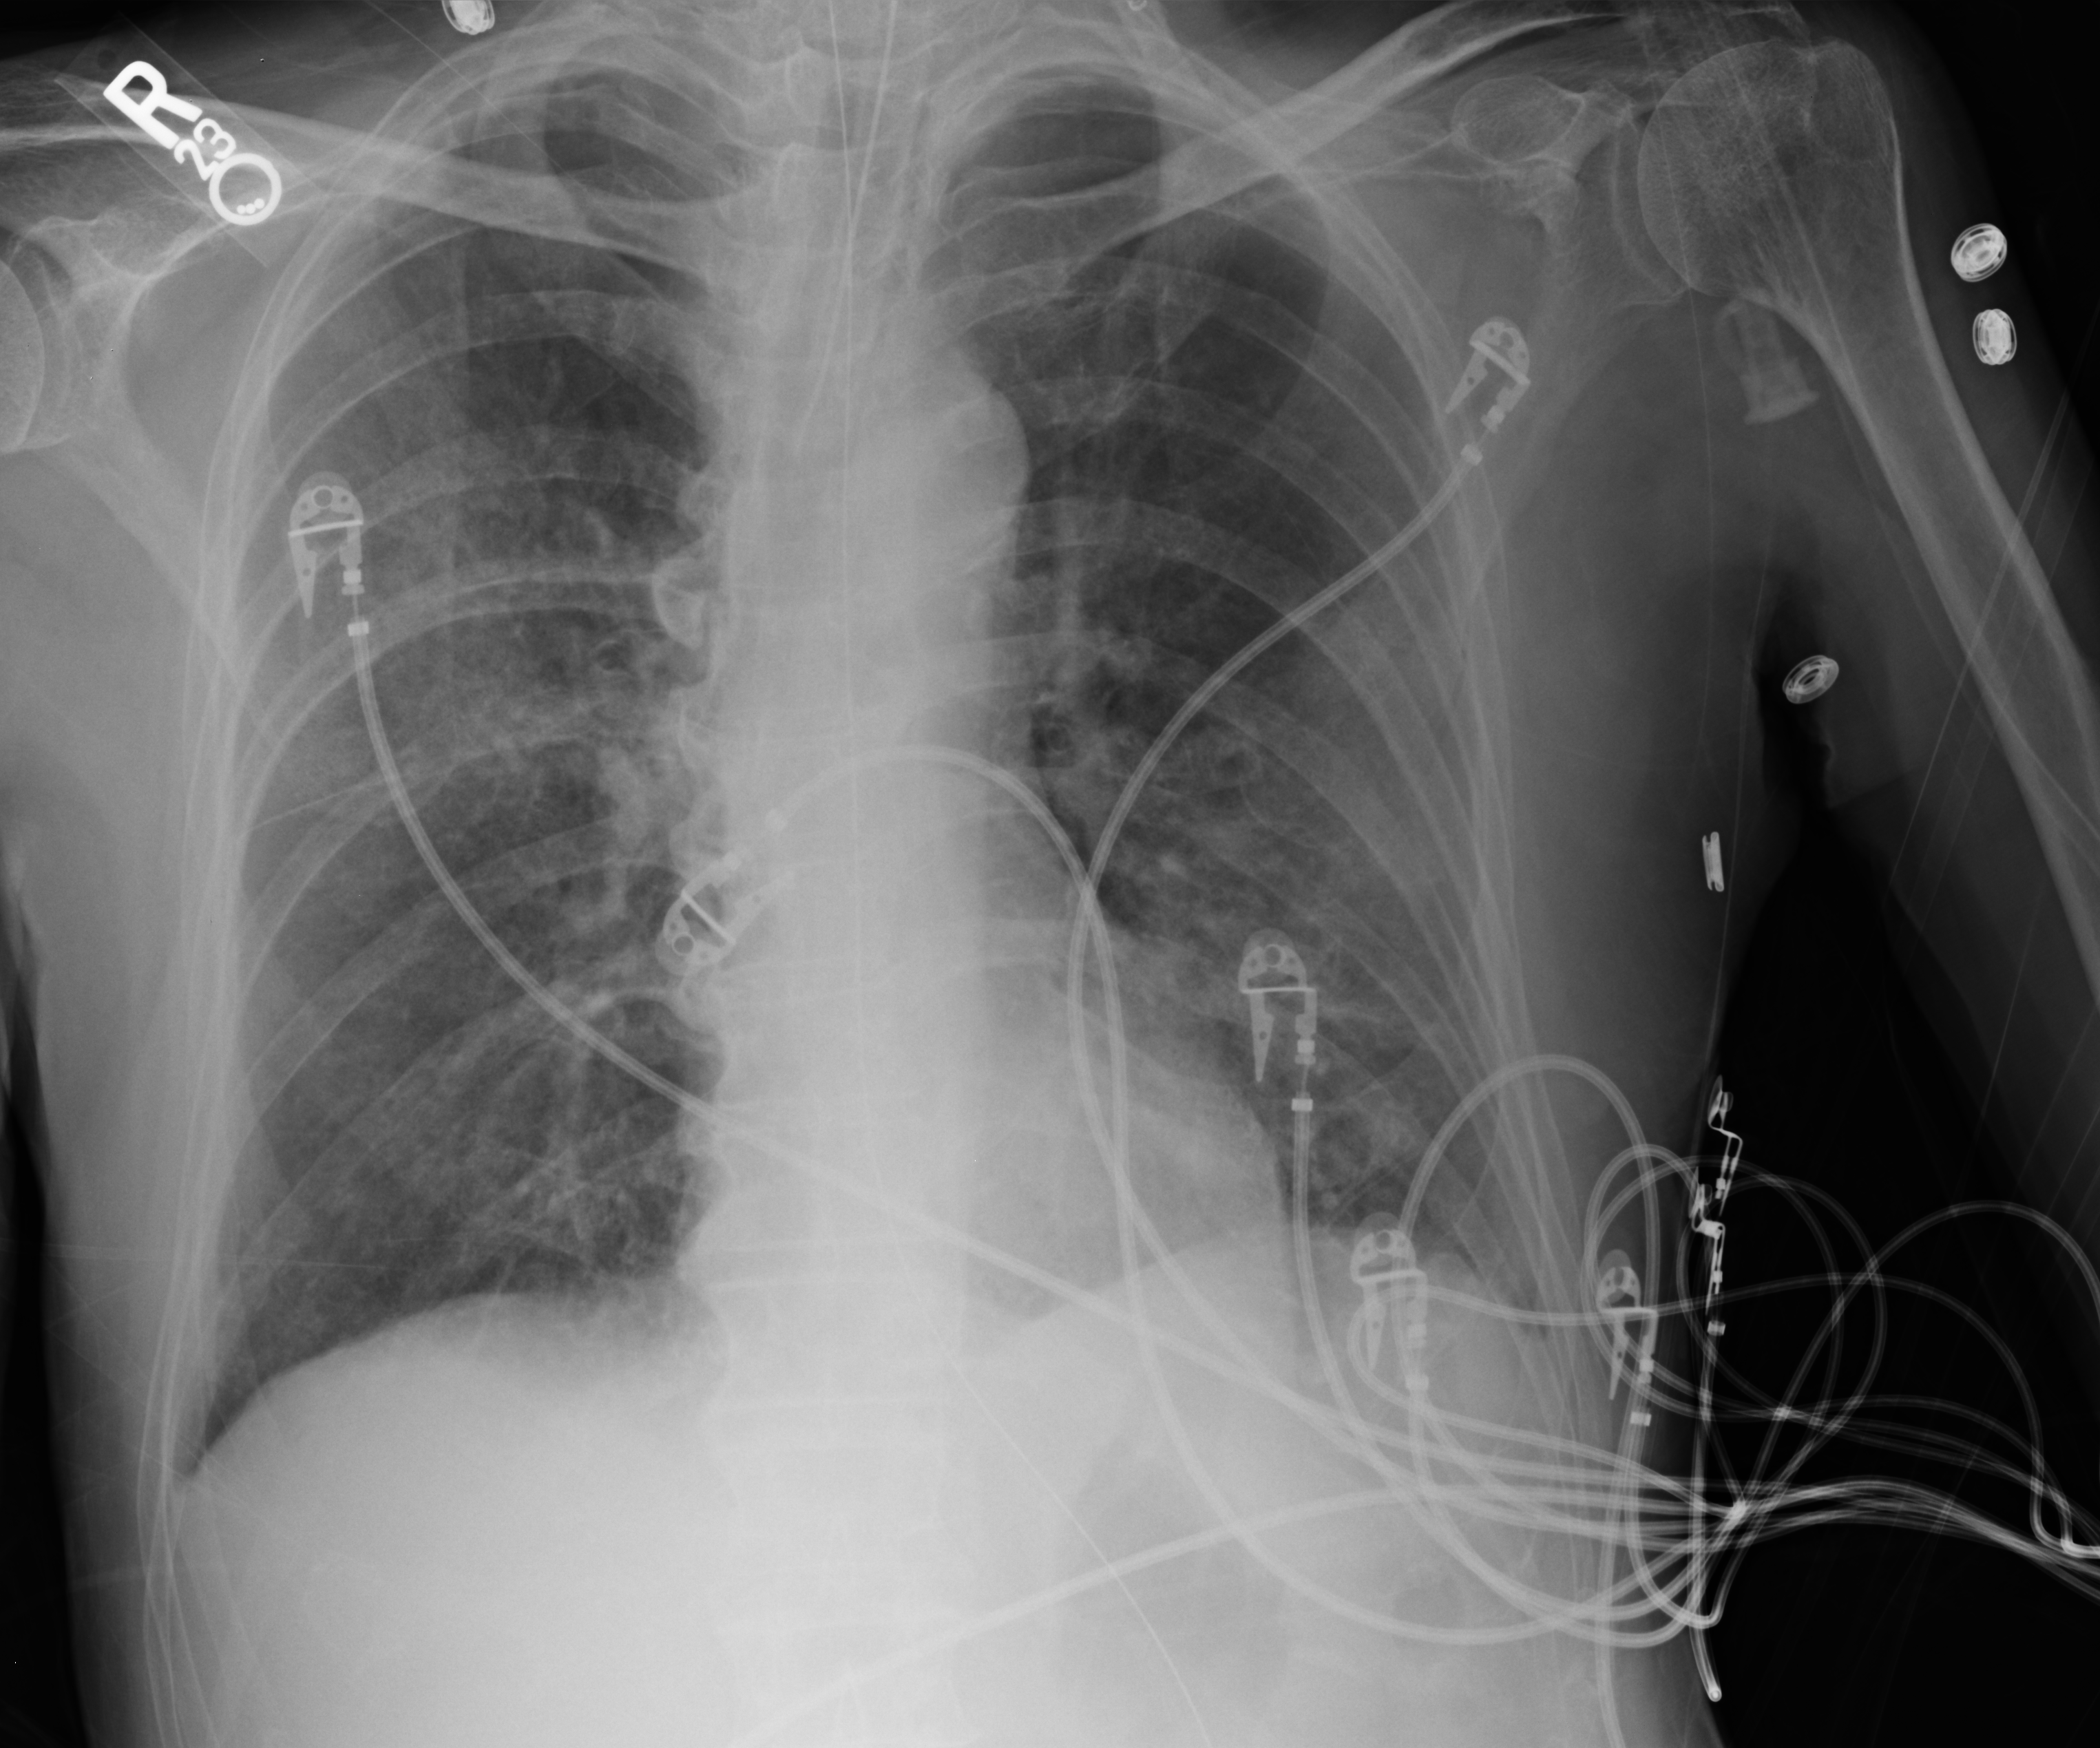
Portable chest radiograph, anteroposterior (AP) projection. Patient hospitalised with COVID-19; male, aged 60–74 years.
Hospital-stay facts (about this admission, not read from this image; timing relative to this image not recorded):
- hypertension (admission record): yes
- admitted to intensive care during this hospital stay: yes
- mechanically ventilated during this hospital stay: yes